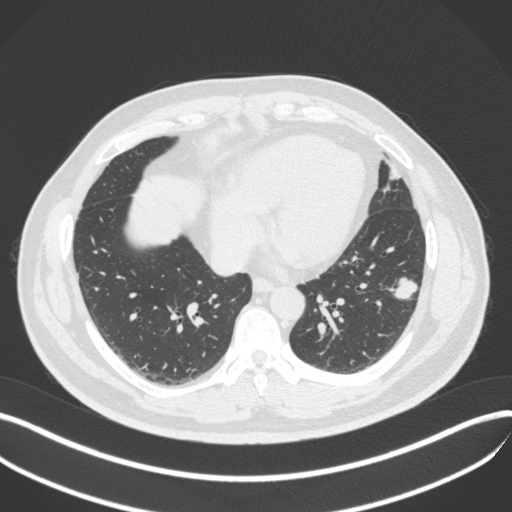
Chest CT, one axial slice. 120 kVp. Lung window (W 1500 / L -600 HU). 1 mm slice thickness. 512 × 512 image matrix, field of view 400 × 400 mm. Patient: male, 39 years. From the clinical record (not read from this slice): clinical TNM (as recorded): T2a N0 M0.
Structures marked on this image (bounding box drawn by a radiologist):
- lung tumour (recorded histology: adenocarcinoma): box from (x=384, y=268) to (x=421, y=305) px